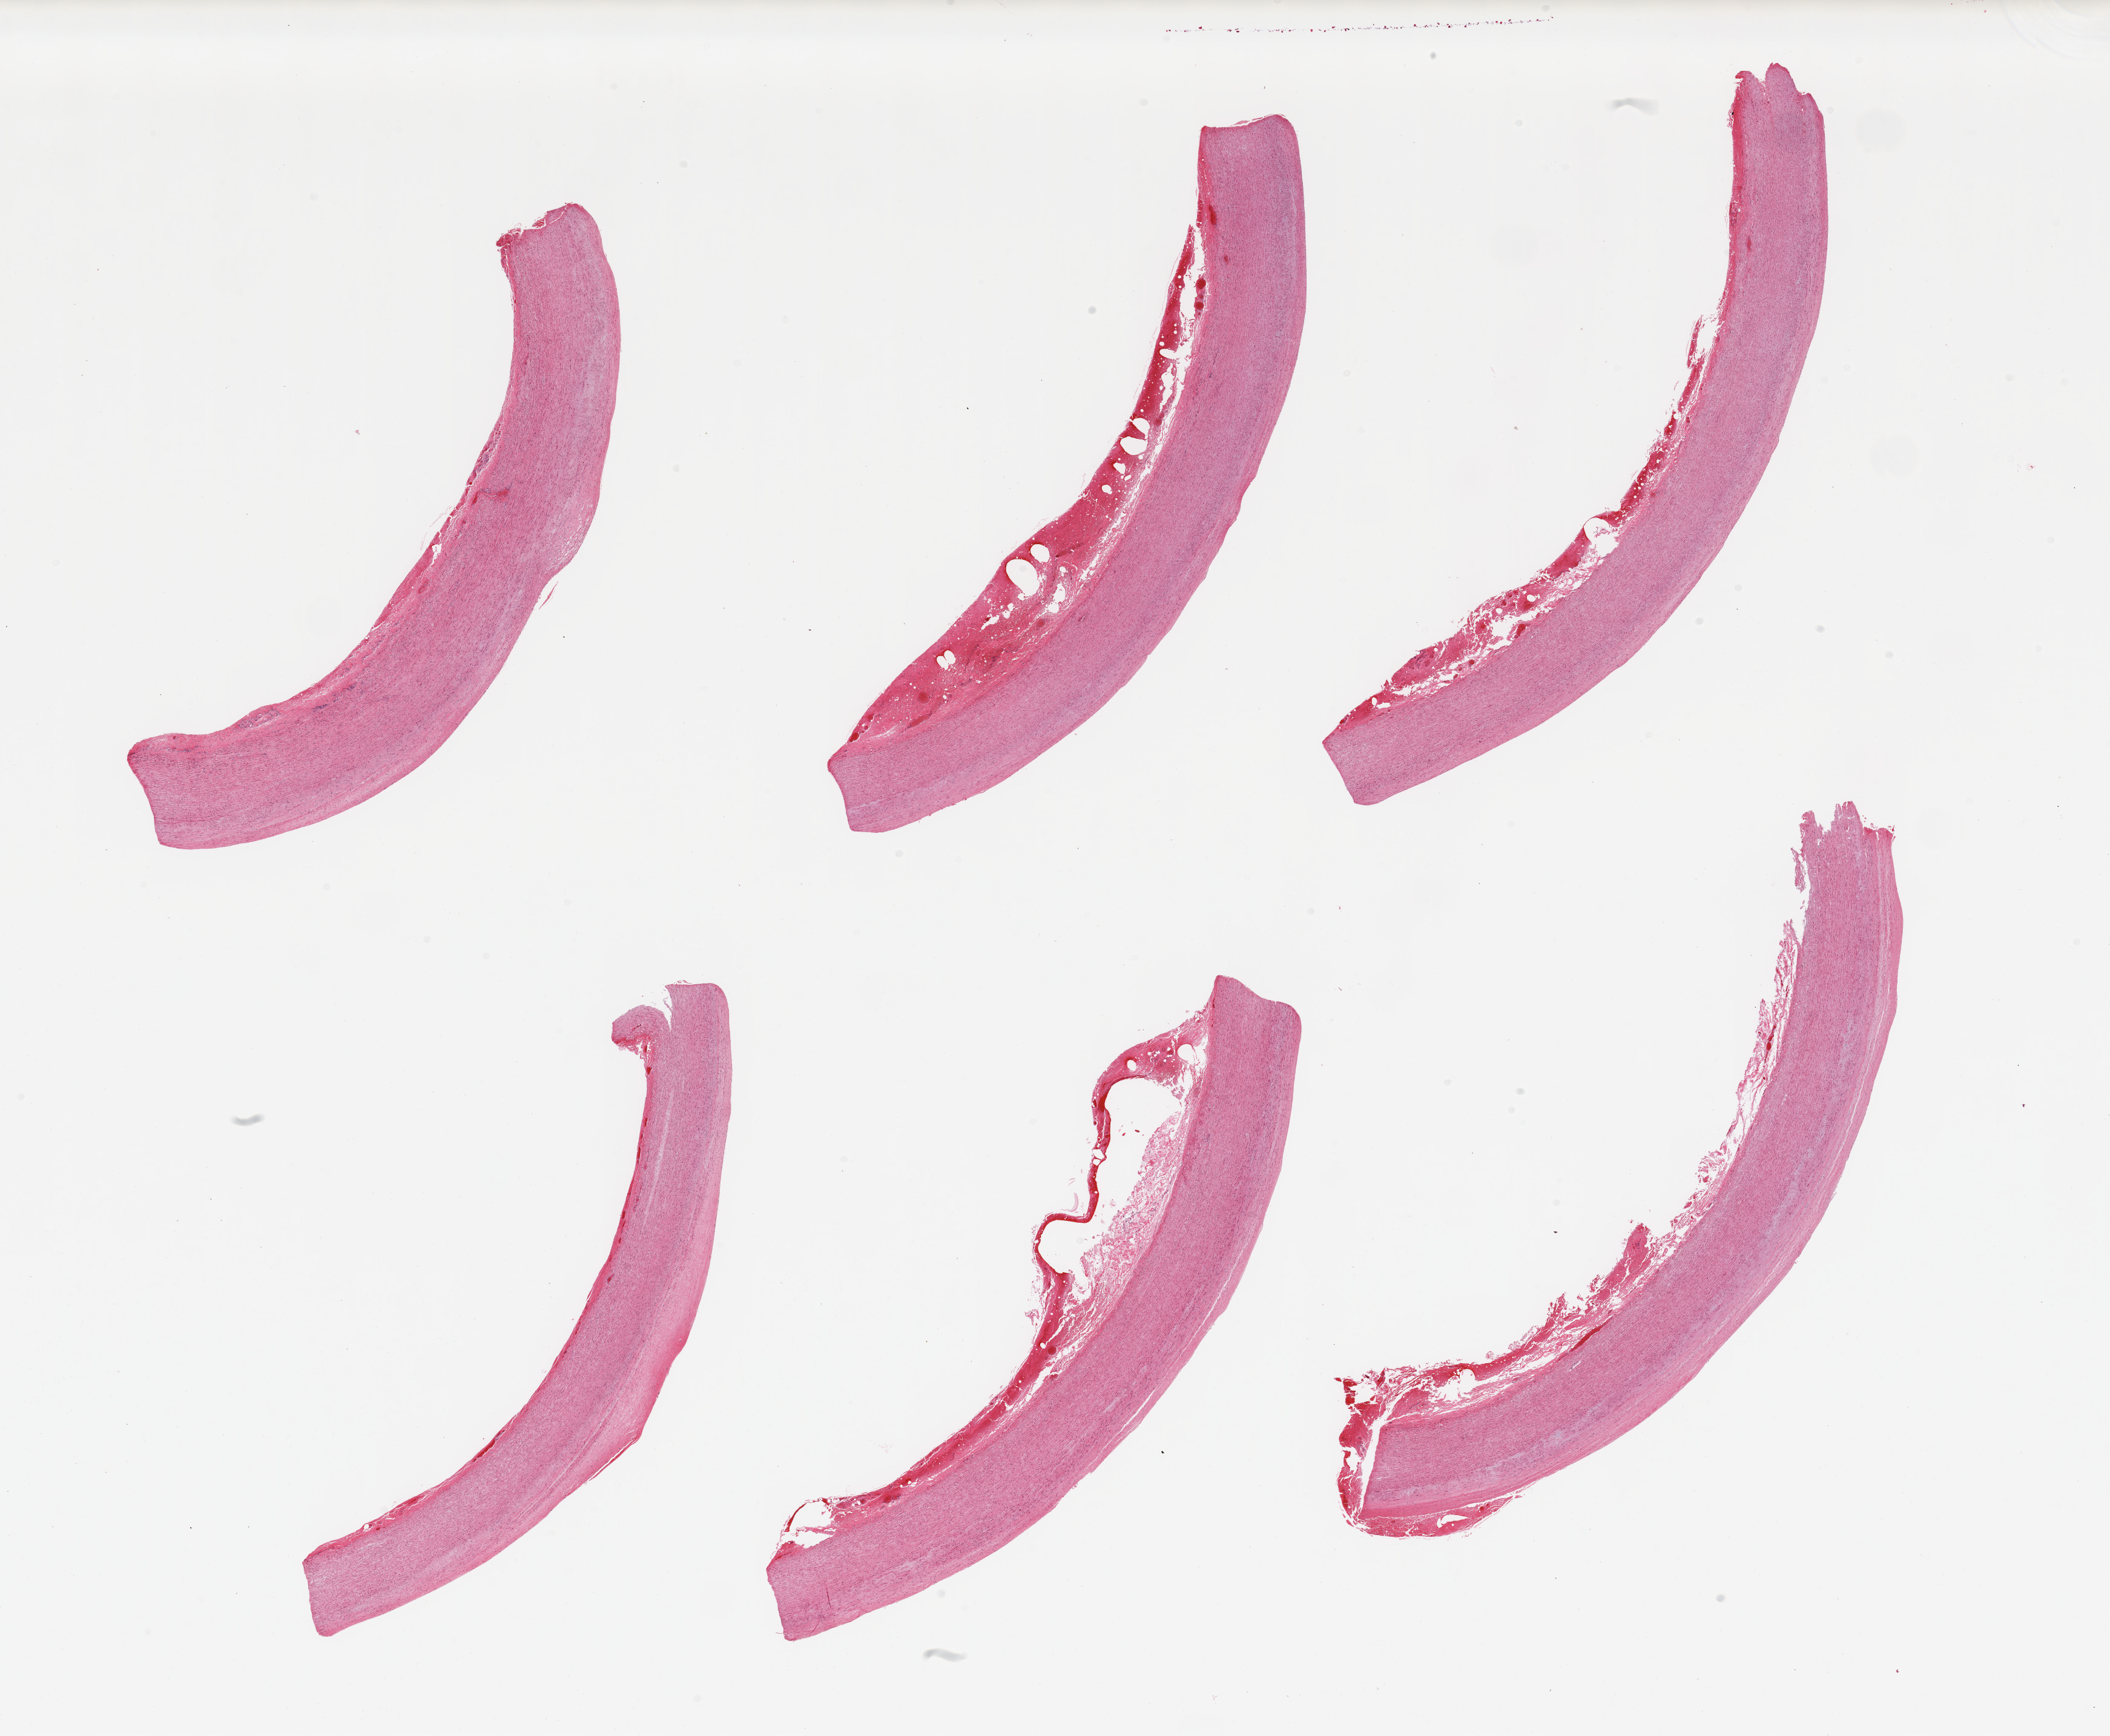
Digitized hematoxylin and eosin (H&E)-stained section, low-resolution overview of the scanned area, about 27.6 x 22.7 mm (slide scanned at 20x); PAXgene-fixed, paraffin-embedded tissue; section of aorta (target tissue); tissue donor sample. Donor sex: male.
Pathologist's review note for this sample: 6 pieces; slight fibrous intimal thickening; adventitial hemorrhage in 4 pieces.